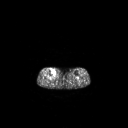
FDG PET of an extremity soft-tissue mass (from a PET/CT study), one axial slice. Position 137 of 267 along the scan axis. 3.27 mm slice thickness. 128 × 128 image matrix, field of view 700 × 700 mm. Female patient, age 65 years. Case-level facts recorded for this patient, not image findings: histological type: undifferentiated – high grade; grade: high; site of the primary tumour: right thigh.
Annotated regions visible in this slice (expert contour drawn on MRI and transferred to this co-registered scan by the dataset authors):
- gross tumour volume (mass): bounding box <51,69,56,75> (left, top, right, bottom; pixels)